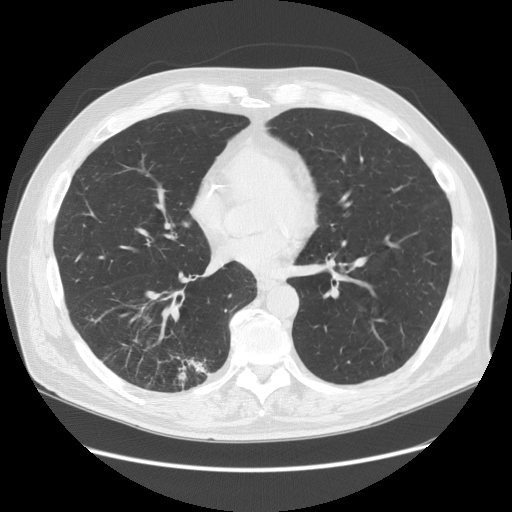
Chest CT (low-dose screening protocol), one axial image. First (baseline) screen. Lung window (W 1500 / L -600 HU). Standard (soft-tissue) reconstruction kernel (STANDARD). 120 kVp. Slice 85 of 149 in the series. Male, age 68 years at enrolment. Former smoker at enrolment.
• Lesion marked by an expert reader, bounding box [x1, y1, x2, y2] px = [122, 330, 226, 405].
• Reader record for this screening exam (exam-level; its link to the box is not recorded): non-calcified nodule or mass ≥4 mm, right lower lobe, 37 × 20 mm, spiculated (stellate) margins, soft tissue attenuation.
• Official screen result: positive, change unspecified: nodule(s) >= 4 mm or enlarging nodule(s), mass(es), or other non-specific abnormalities suspicious for lung cancer.
• Later outcome: lung cancer diagnosed 24 days after this screen — adenosquamous carcinoma, right lower lobe, poorly differentiated (G3), stage IIIA (AJCC 6th edition), 30 mm at pathology.